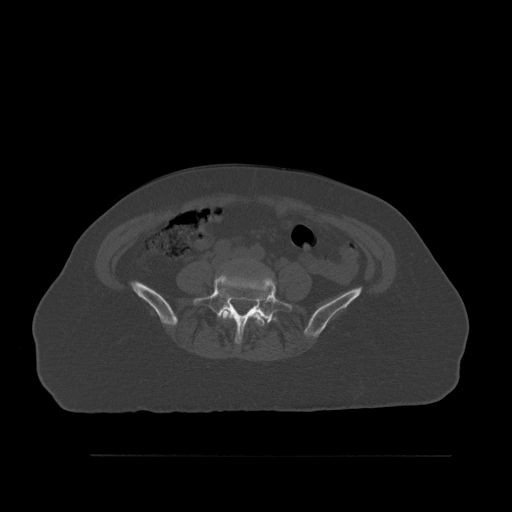
CT including the spine, one axial slice. Position 193 of 527 along the scan axis. Bone window (W 1800 / L 400 HU). 1.5 mm slice thickness. 512 × 512 image matrix, field of view 470 × 470 mm. Patient: female, 73 years. From the clinical record (not read from this slice): primary cancer: breast; vertebrae with lytic lesions (as recorded): L2.
Outlined on this slice (semi-automatically segmented with operator editing):
- L4 vertebra: box from (x=222, y=306) to (x=265, y=328) px
- L5 vertebra: (x=193, y=274)–(x=292, y=344)